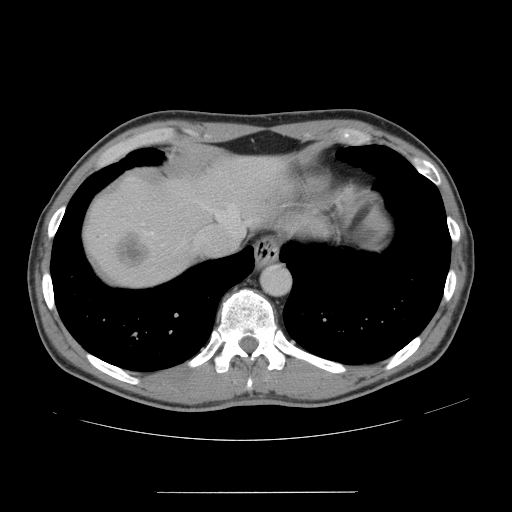
Contrast-enhanced abdominal CT, one axial slice; position 134 of 178 along the scan axis; 120 kVp; soft-tissue window (W 400 / L 40 HU); 2.5 mm slice thickness; 512 × 512 image matrix, field of view 401 × 401 mm. Male patient, age 53 years. From the clinical record (not read from this slice): diagnosis: colorectal cancer liver metastases, imaged before liver resection; multiple liver metastases: yes; largest metastasis: 2.4 cm; disease in both lobes: no.
Annotated regions visible in this slice (outlined manually by an expert reader):
- hepatic veins: bounding box (x1, y1, x2, y2) in pixels: (150, 202, 249, 238)
- liver: (85, 157, 281, 284)
- planned liver remnant (the part of the liver to remain after resection): (181, 157, 283, 221)
- liver metastasis: (116, 233, 150, 268)